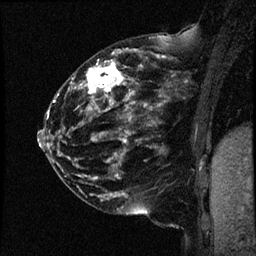
Breast MRI (dynamic contrast-enhanced), one sagittal slice; position 21 of 44 along the scan axis; dynamic contrast-enhanced study with each time point stored as its own series, time point 2 of 4 at this slice position (early post-contrast, ordered by acquisition time); 1.5 T; TE 4.2 ms, TR 17.7 ms; 2 mm slice thickness; 256 × 256 image matrix, field of view 200 × 200 mm. Patient: female, 52 years. From the clinical record (not read from this slice): setting: breast cancer imaged before/during neoadjuvant chemotherapy; receptor status: HR-positive, HER2-negative.
Outlined on this slice (semi-automatically segmented with operator editing):
- analysis volume of interest (the breast-tissue region the enhancement analysis was run in; not a lesion): bounding box <47,48,163,147> (left, top, right, bottom; pixels)
- tumour enhancement mask (voxels above the 100 % enhancement threshold inside the analysis volume of interest): <71,51,152,143>